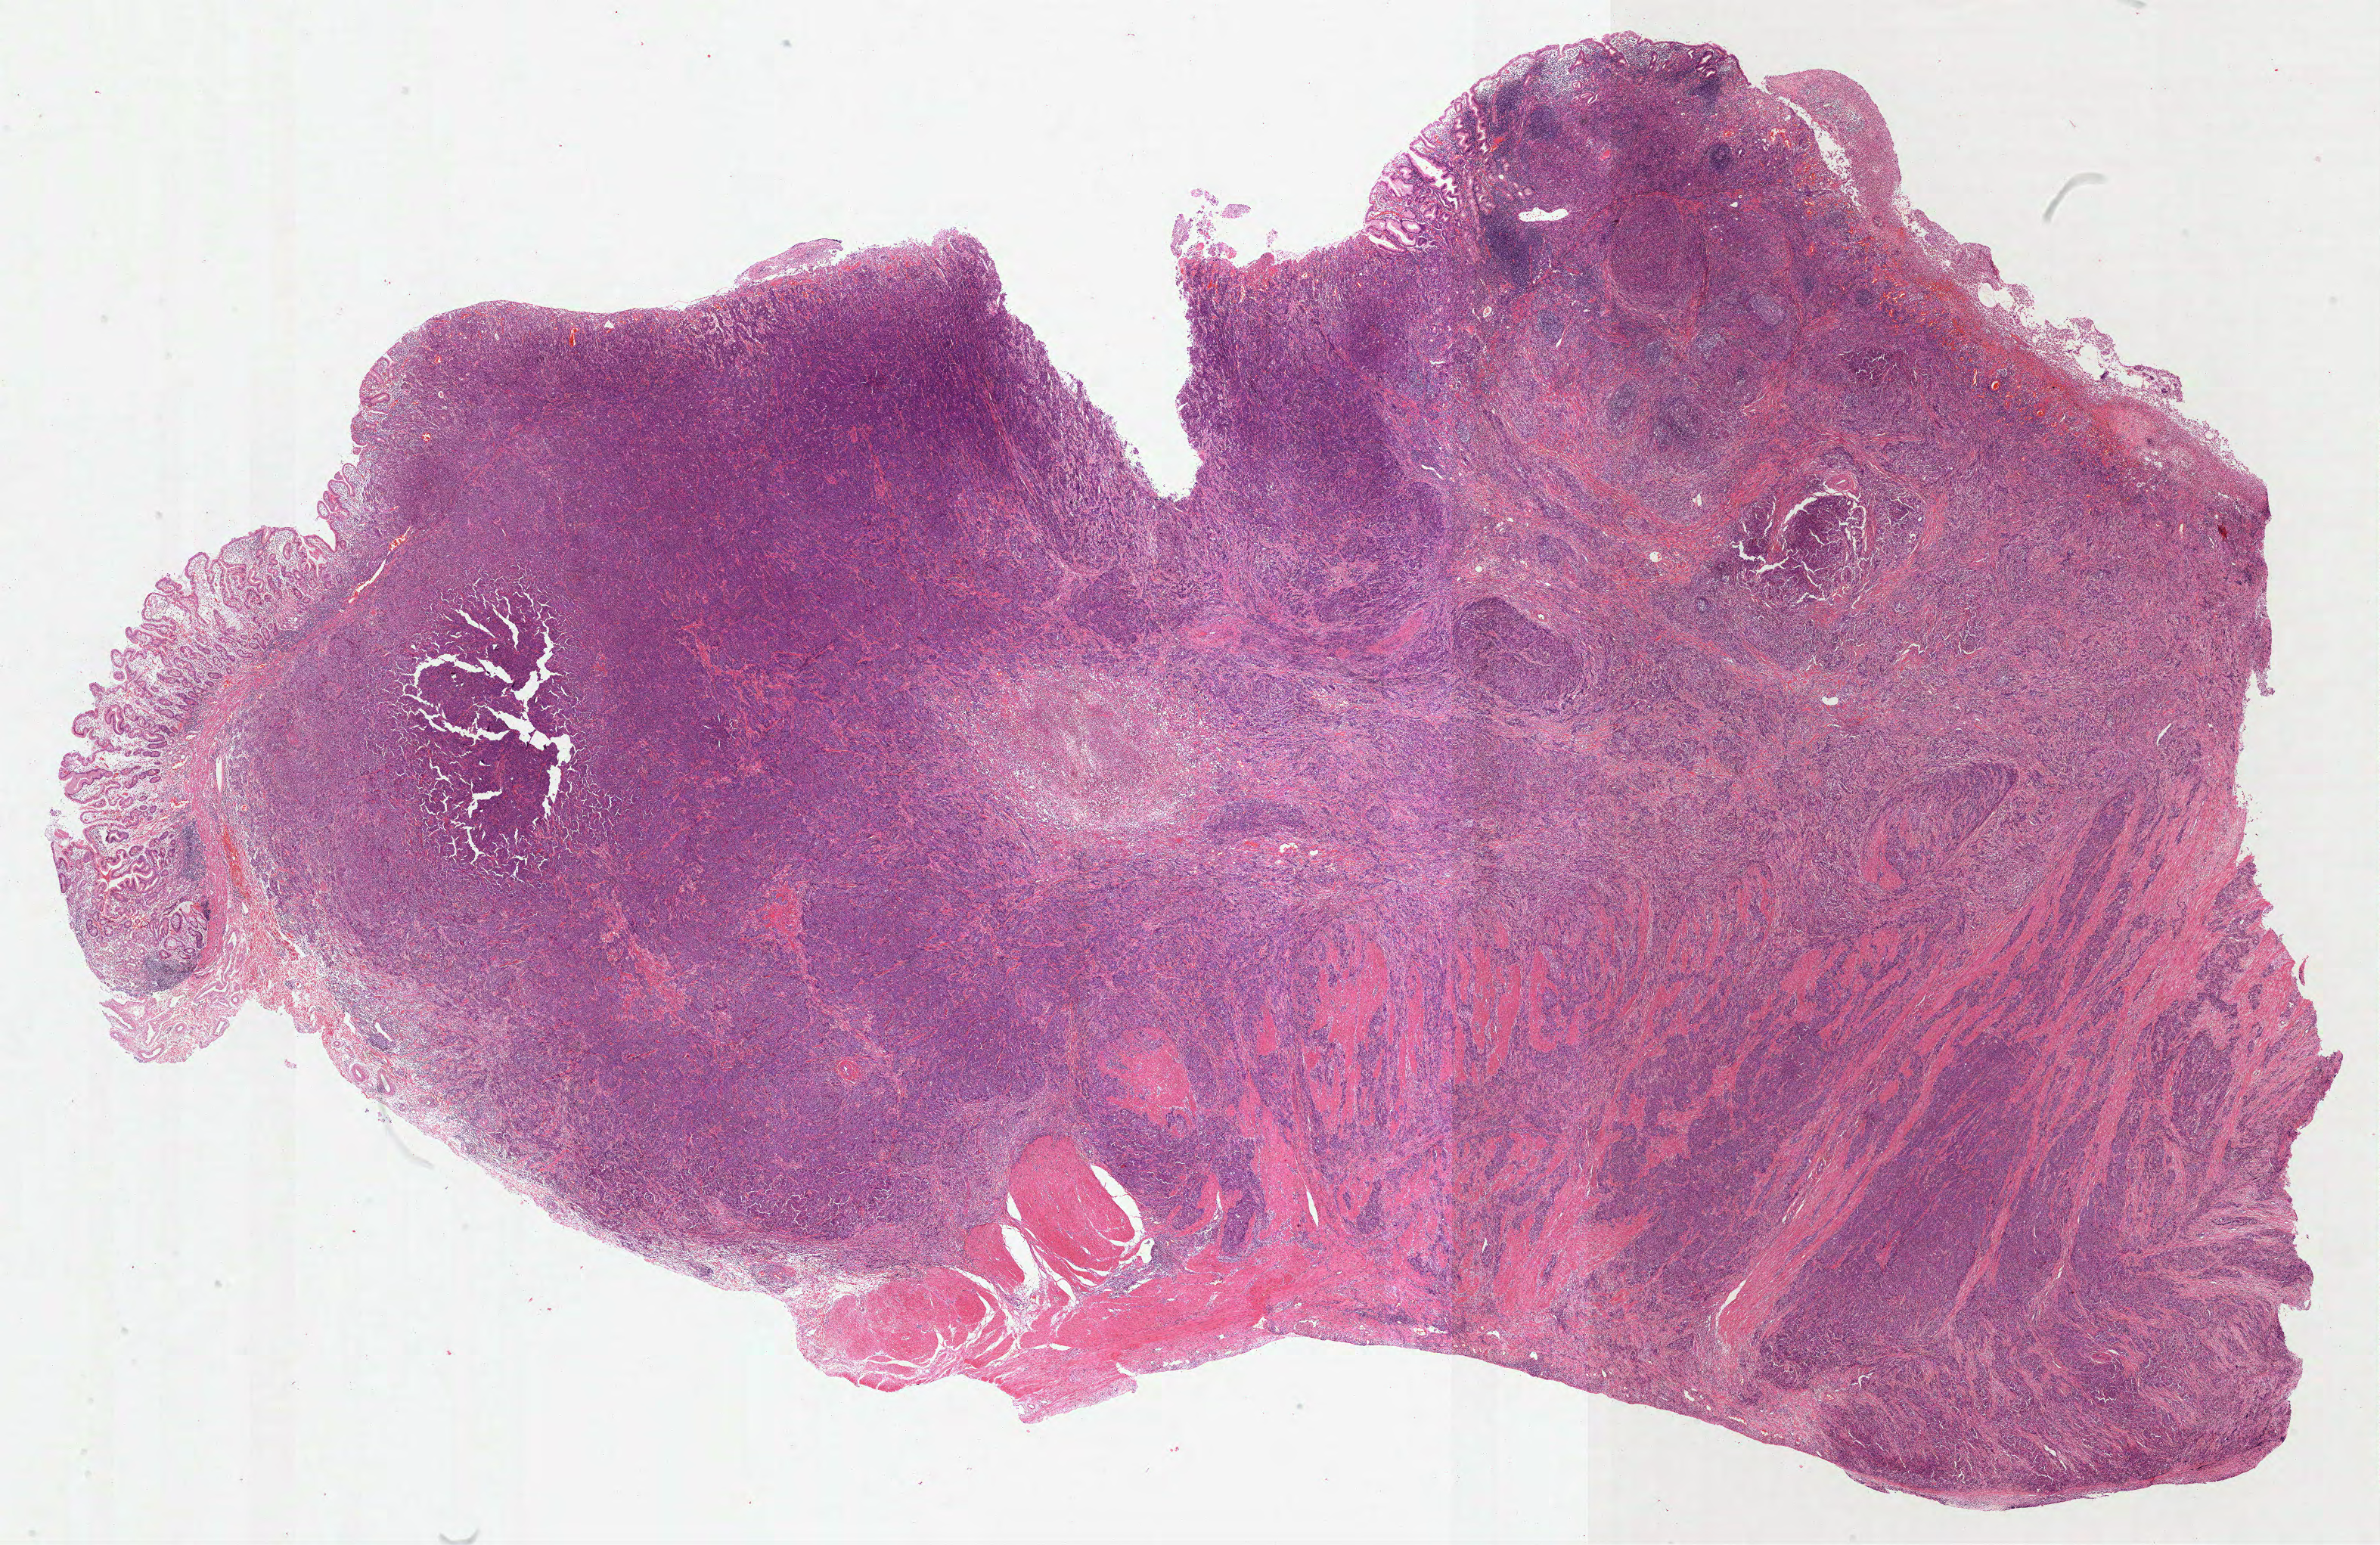
Hematoxylin and eosin (H&E) stained whole-slide image, whole scanned area (about 25.4 x 16.5 mm, from a 40x scan) shown as a low-resolution overview. Formalin-fixed paraffin-embedded (FFPE) diagnostic section. Sample: primary tumour, stomach. Male, age 51 years at initial diagnosis. Histologic grade: G3 (poorly differentiated).
• diagnosis: Adenocarcinoma, NOS
• TNM: T3 N1 M0
• lymph nodes positive (case pathology): 1 of 15 examined
• AJCC pathologic stage: IIB (7th edition)